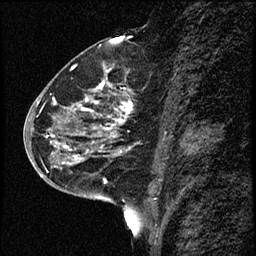
Breast MRI (dynamic contrast-enhanced), one sagittal slice; slice 32 of 68 in the series (ordered by position); dynamic contrast-enhanced study with each time point stored as its own series, time point 2 of 3 at this slice position (early post-contrast, ordered by acquisition time); 1.5 T; TE 4.2 ms, TR 17.6 ms; 2 mm slice thickness; 256 × 256 image matrix, field of view 200 × 200 mm. Female patient, age 52 years. Case-level facts recorded for this patient, not image findings: setting: breast cancer imaged before/during neoadjuvant chemotherapy; receptor status: HER2-positive.
Outlined on this slice (semi-automatic segmentation, software-assisted and operator-edited):
- analysis volume of interest (the breast-tissue region the enhancement analysis was run in; not a lesion): bounding box [x1, y1, x2, y2] px = [50, 61, 132, 184]
- tumour enhancement mask (voxels above the 100 % enhancement threshold inside the analysis volume of interest): [53, 80, 130, 164]